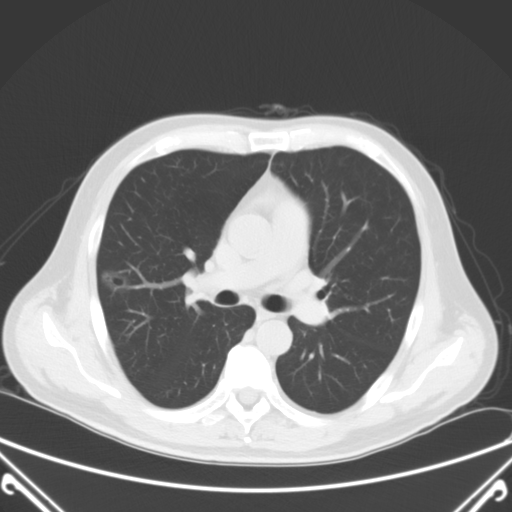
Chest CT, one axial slice. Position 45 of 72 along the scan axis. 120 kVp. Lung window (W 1500 / L -600 HU). 512 × 512 image matrix, field of view 380 × 380 mm. Male patient, age 64 years. Case-level facts recorded for this patient, not image findings: clinical TNM (as recorded): T1c N0 M0; histopathological grade: G2.
Outlined on this slice (bounding box drawn by a radiologist):
- lung tumour (recorded histology: adenocarcinoma): box from (x=97, y=259) to (x=137, y=300) px